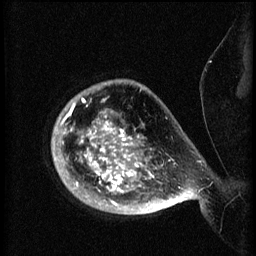
Breast MRI (dynamic contrast-enhanced), one sagittal slice; position 56 of 60 along the scan axis; 3 images stored at this slice position (order not interpretable as contrast timing); 1.5 T; TE 4.2 ms, TR 8.2 ms; 2 mm slice thickness; 256 × 256 image matrix, field of view 200 × 200 mm. Patient: female, 50 years.
Structures marked on this image (semi-automatically segmented with operator editing):
- analysis volume of interest (the breast-tissue region the enhancement analysis was run in; not a lesion): box from (x=53, y=80) to (x=173, y=215) px
- tumour enhancement mask (voxels above the 70 % enhancement threshold inside the analysis volume of interest): (x=57, y=98)–(x=173, y=209)